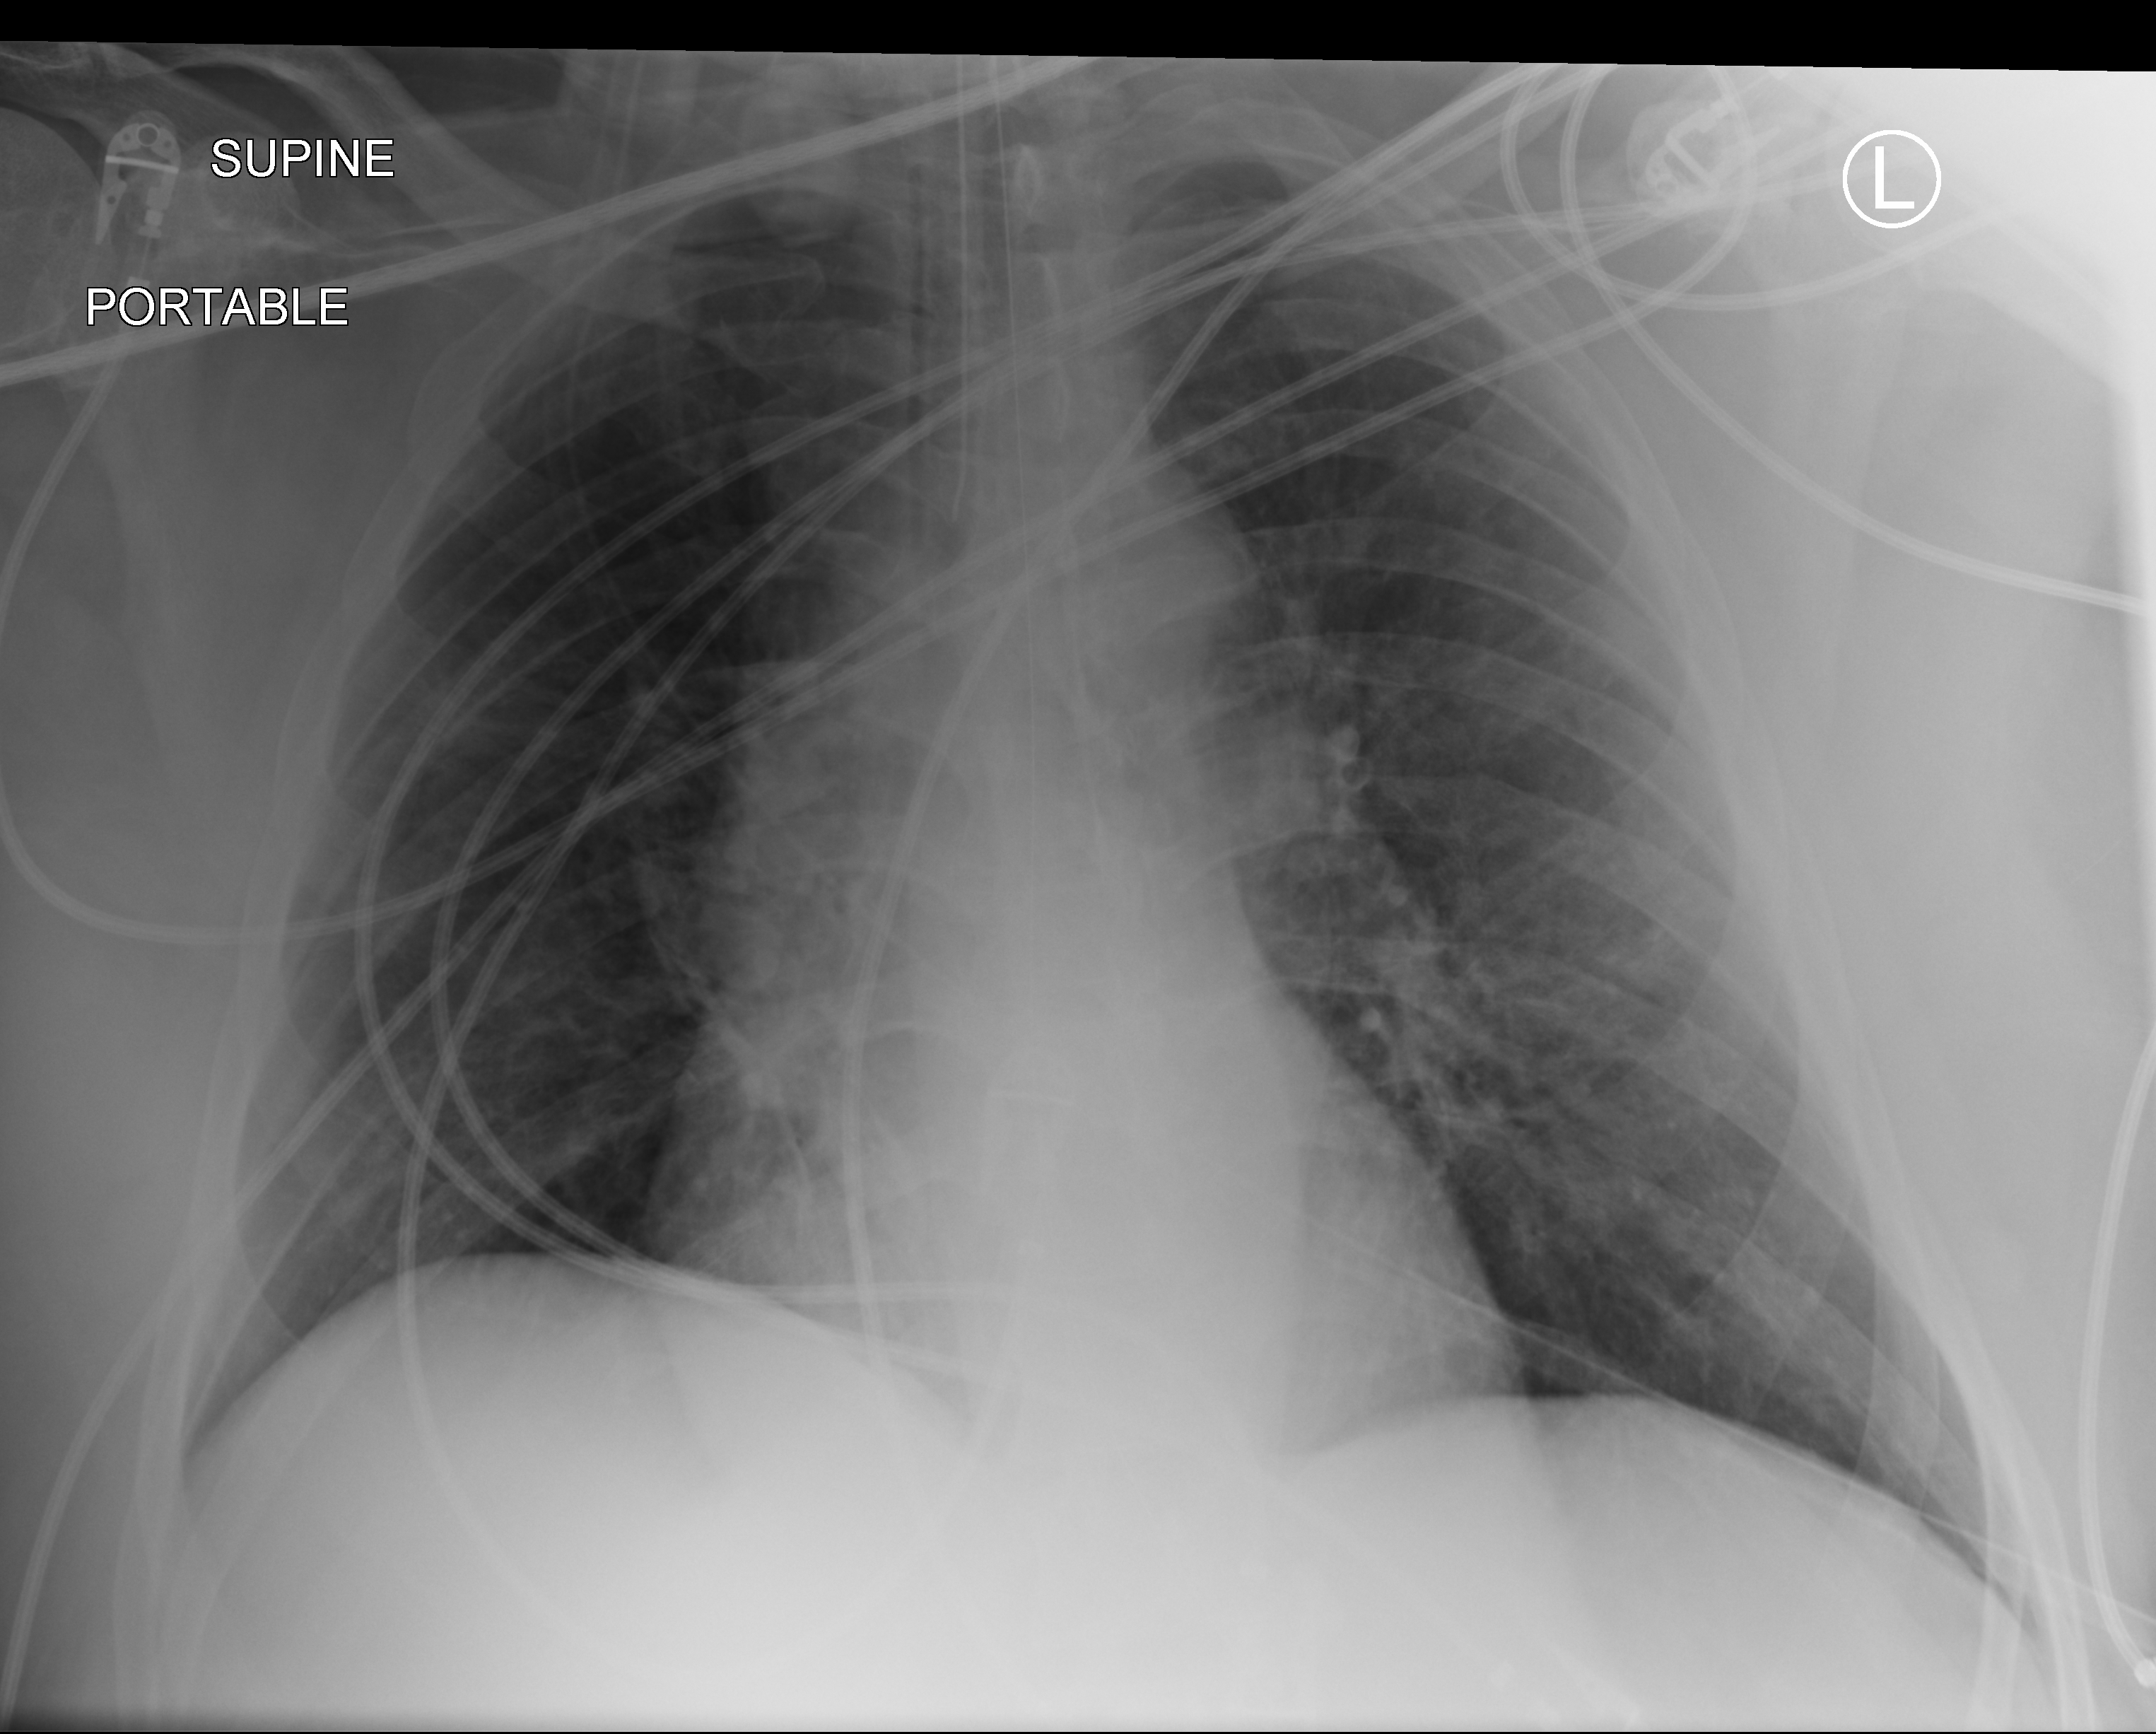
Bedside chest radiograph (computed radiography), anteroposterior (AP) projection. Patient hospitalised with COVID-19; male, aged 60–74 years.
Admission-level facts for this patient (not findings on this image; timing relative to this image not recorded):
- mechanically ventilated during this hospital stay: yes